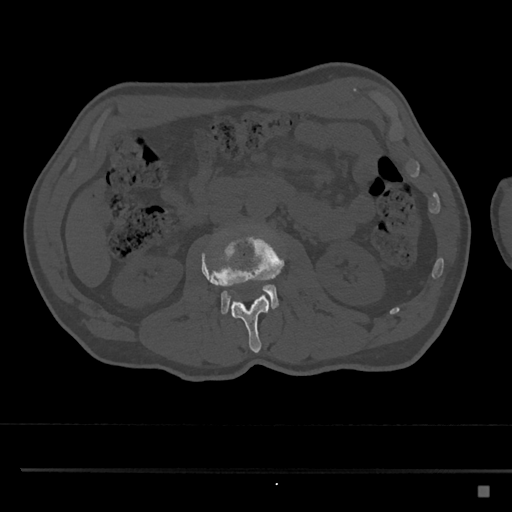
CT including the spine, one axial slice; slice 737 of 797 in the series (ordered by position); reconstruction kernel Br40s/3; bone window (W 1800 / L 400 HU); 0.5 mm slice thickness; 512 × 512 image matrix, field of view 391 × 391 mm. Patient: male, 59 years. Case-level facts recorded for this patient, not image findings: primary cancer: prostate.
Annotated regions visible in this slice (semi-automatically segmented with operator editing):
- L2 vertebra: bounding box [x1, y1, x2, y2] px = [201, 233, 284, 353]
- L3 vertebra: [201, 266, 280, 315]